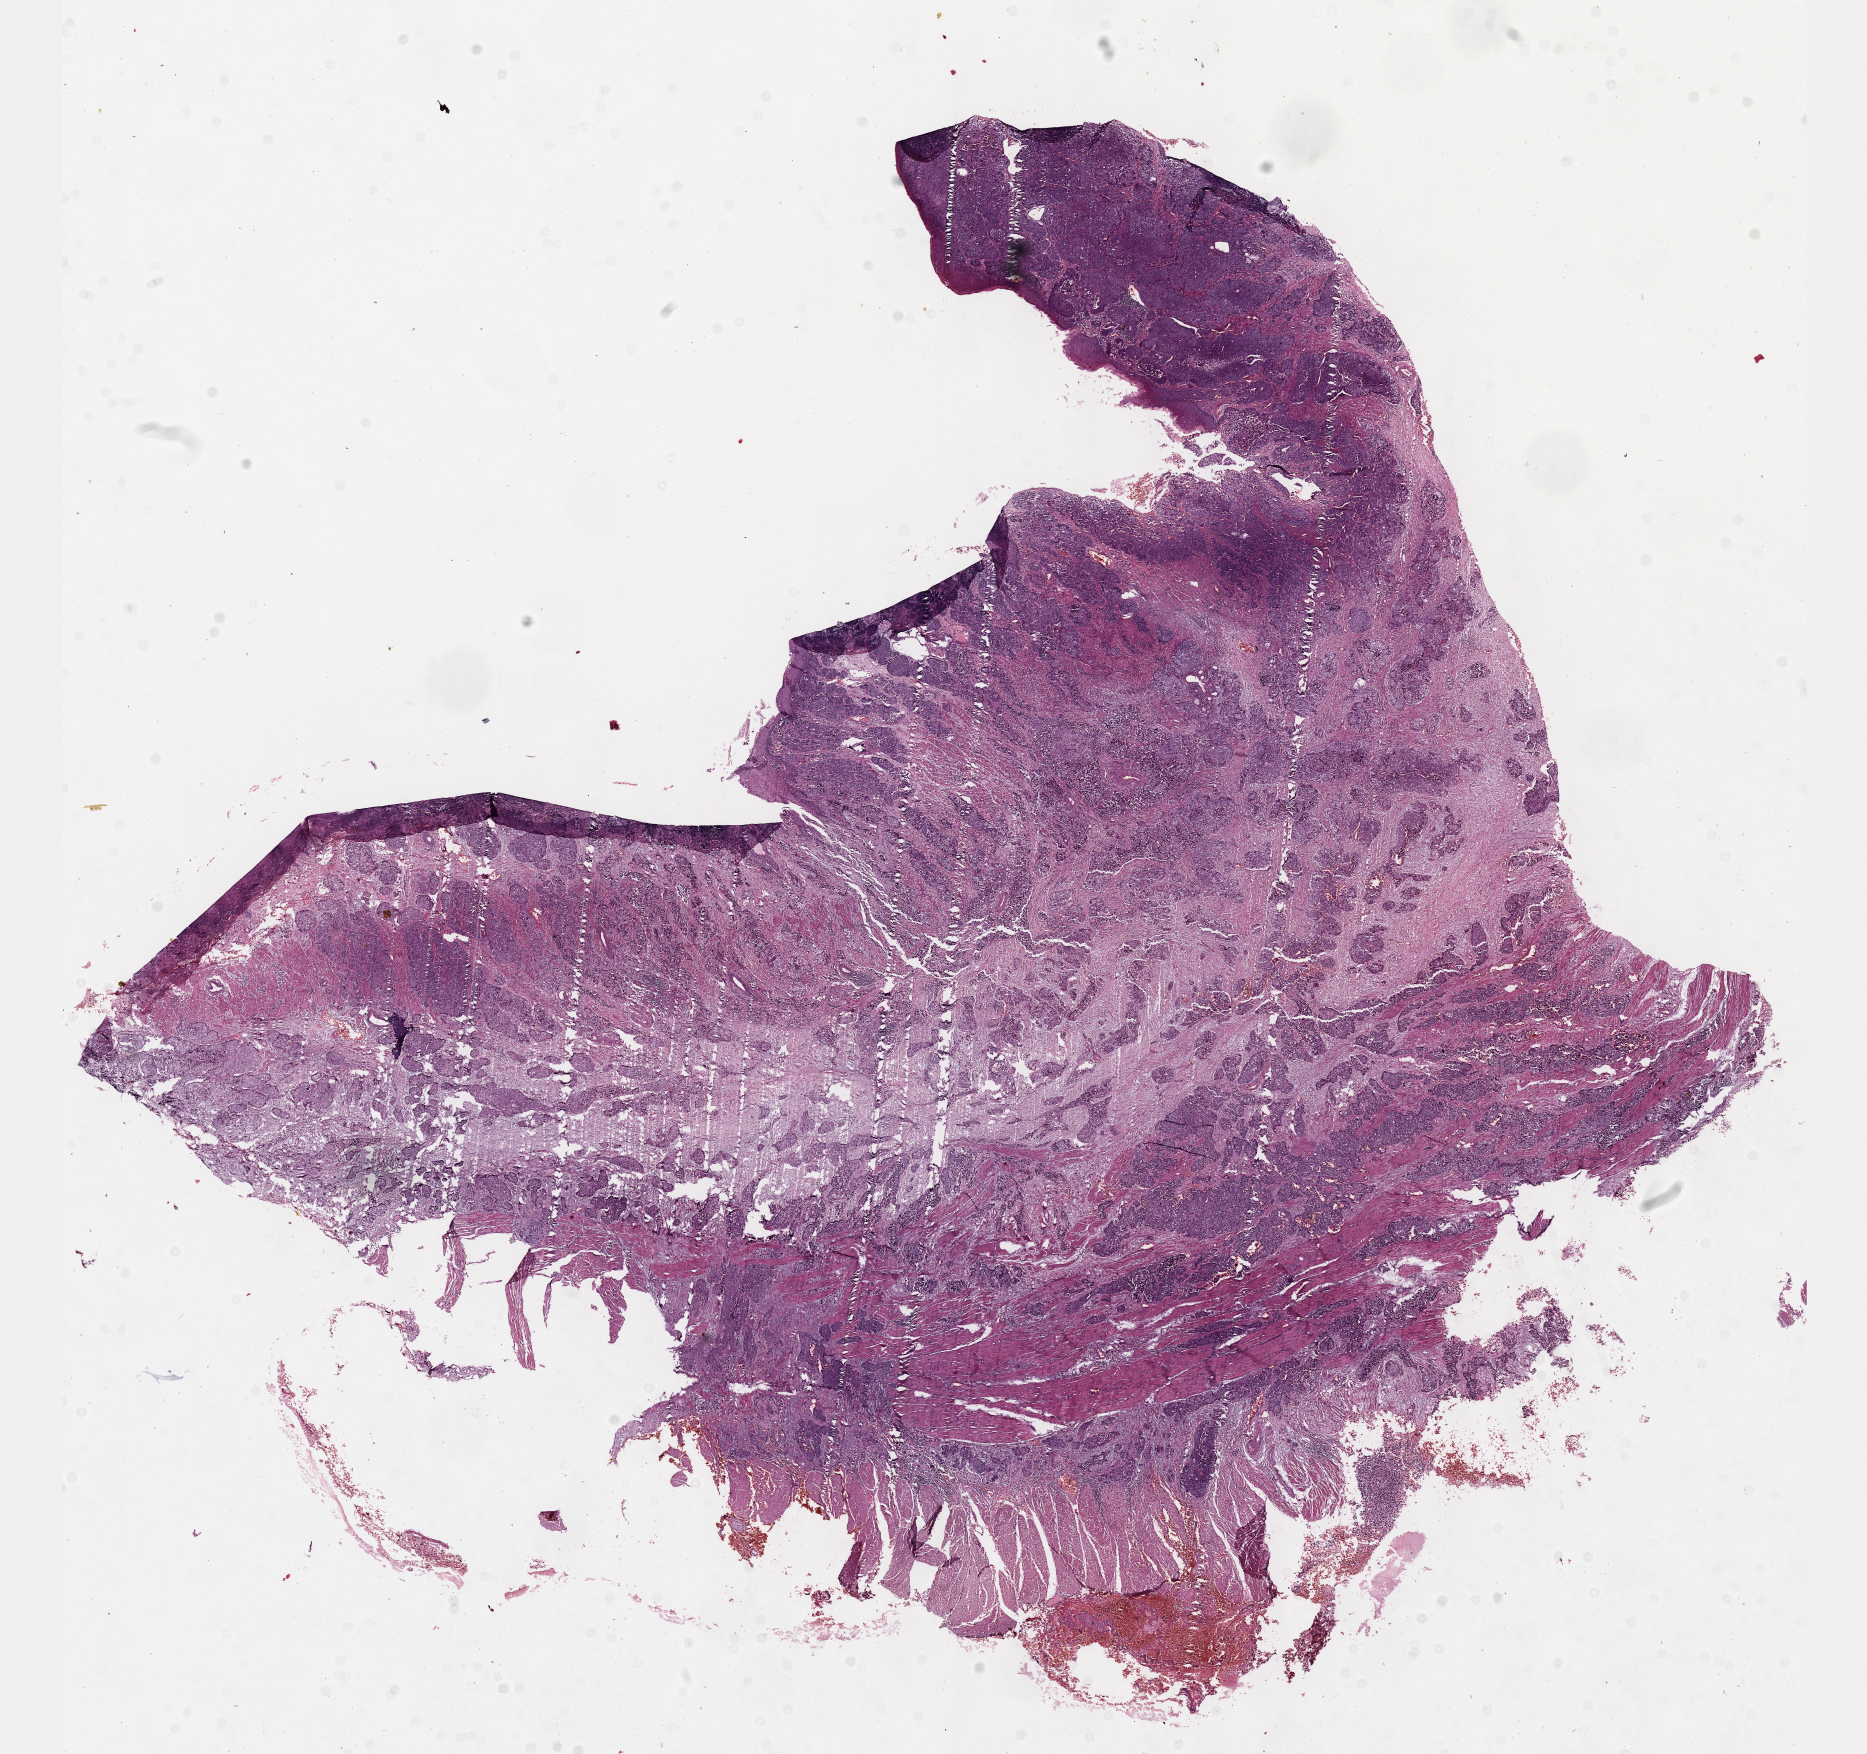
Hematoxylin and eosin (H&E) stained whole-slide image — whole scanned area (about 15.1 x 14.2 mm) shown as a low-resolution overview. FFPE section. Esophagus, primary tumour sample. Patient: male, age at initial diagnosis 62 years. Histologic grade: G3 (poorly differentiated).
- histologic diagnosis: Squamous cell carcinoma, NOS (middle third of esophagus)
- TNM: T3 N0 M0
- AJCC pathologic stage: IIA (6th edition)